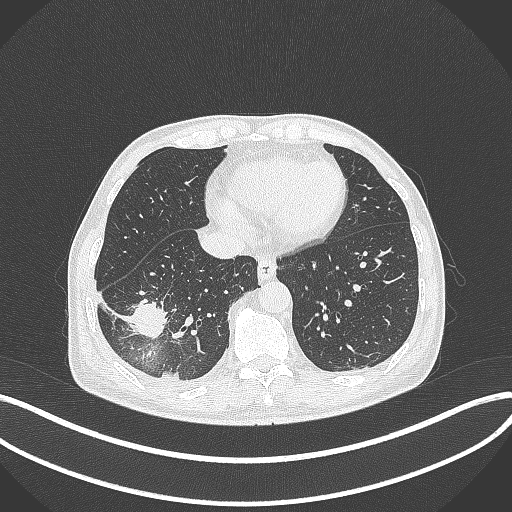
Chest CT, one axial slice; slice 107 of 388 in the series (ordered by position); lung window (W 1500 / L -600 HU); 512 × 512 image matrix, field of view 400 × 400 mm. Patient: male, 64 years. From the clinical record (not read from this slice): clinical TNM (as recorded): T3 N0 M0.
Annotated regions visible in this slice (rectangle marked by the reading radiologist):
- lung tumour (recorded histology: adenocarcinoma): bounding box <128,290,167,345> (left, top, right, bottom; pixels)